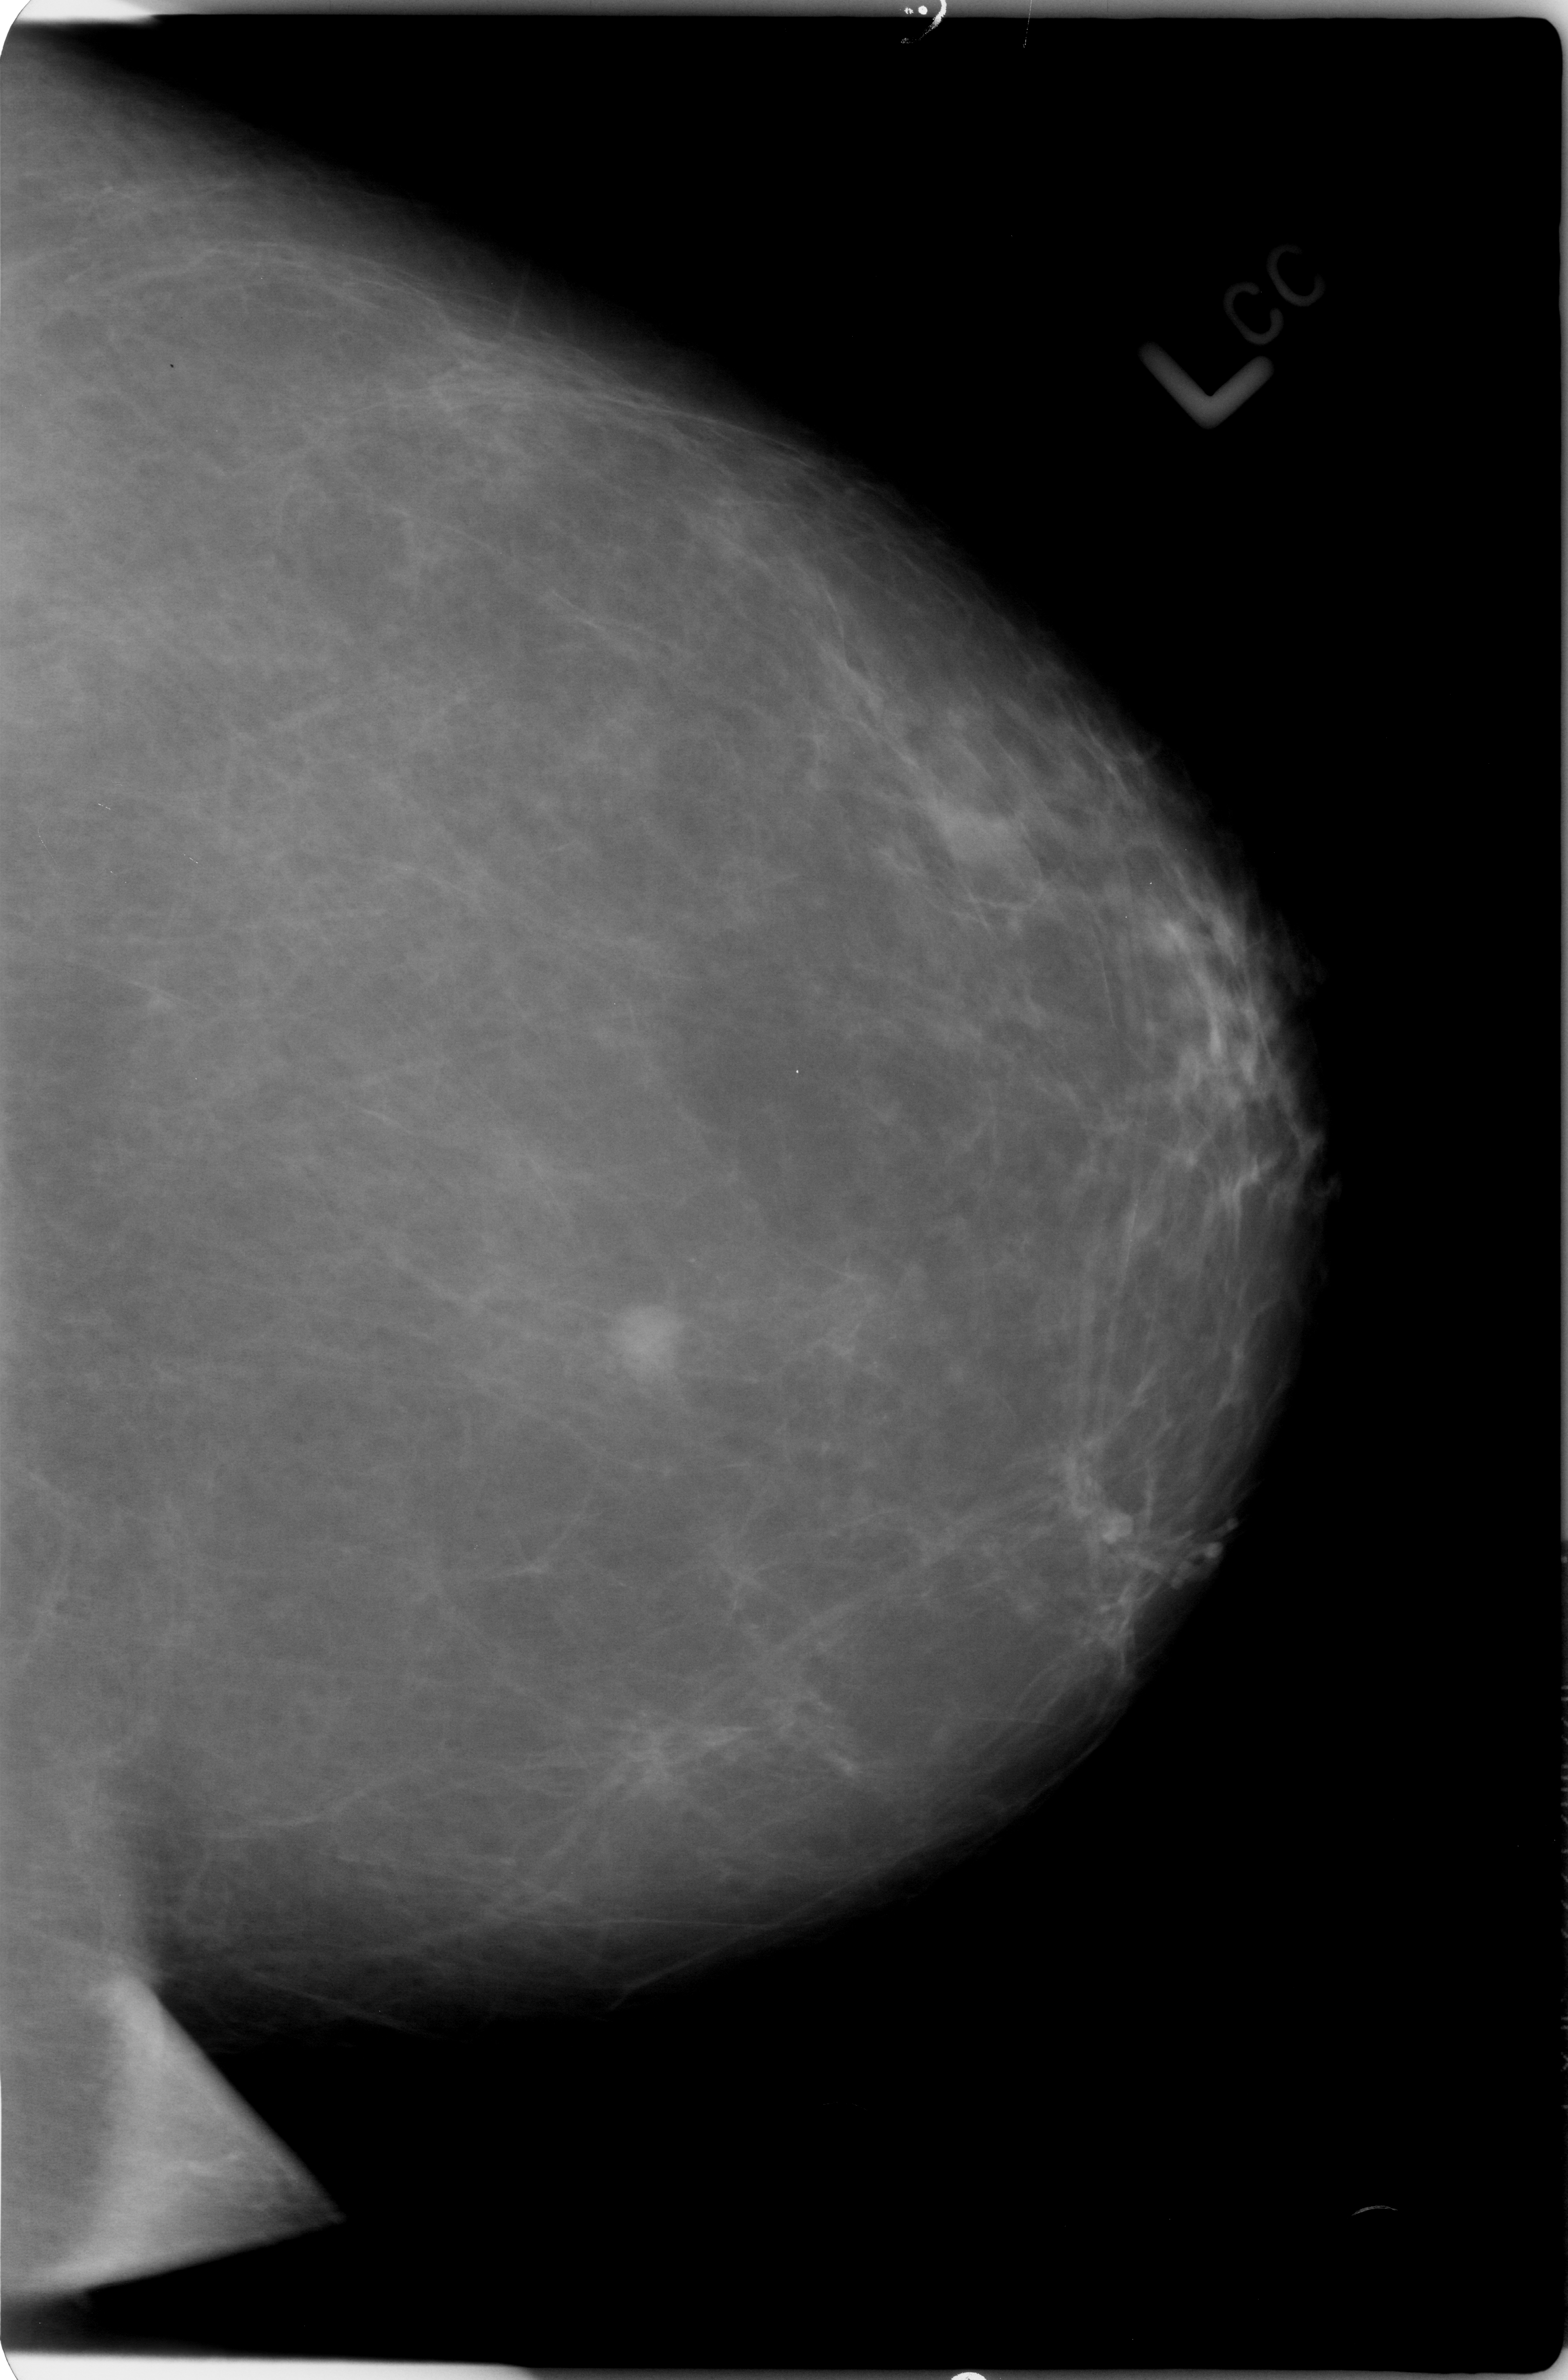
Mammogram (digitized film); left breast; CC view.
- Marked abnormality: mass, shape lobulated, margins ill defined; BI-RADS assessment category 4; pathology (as recorded): malignant.